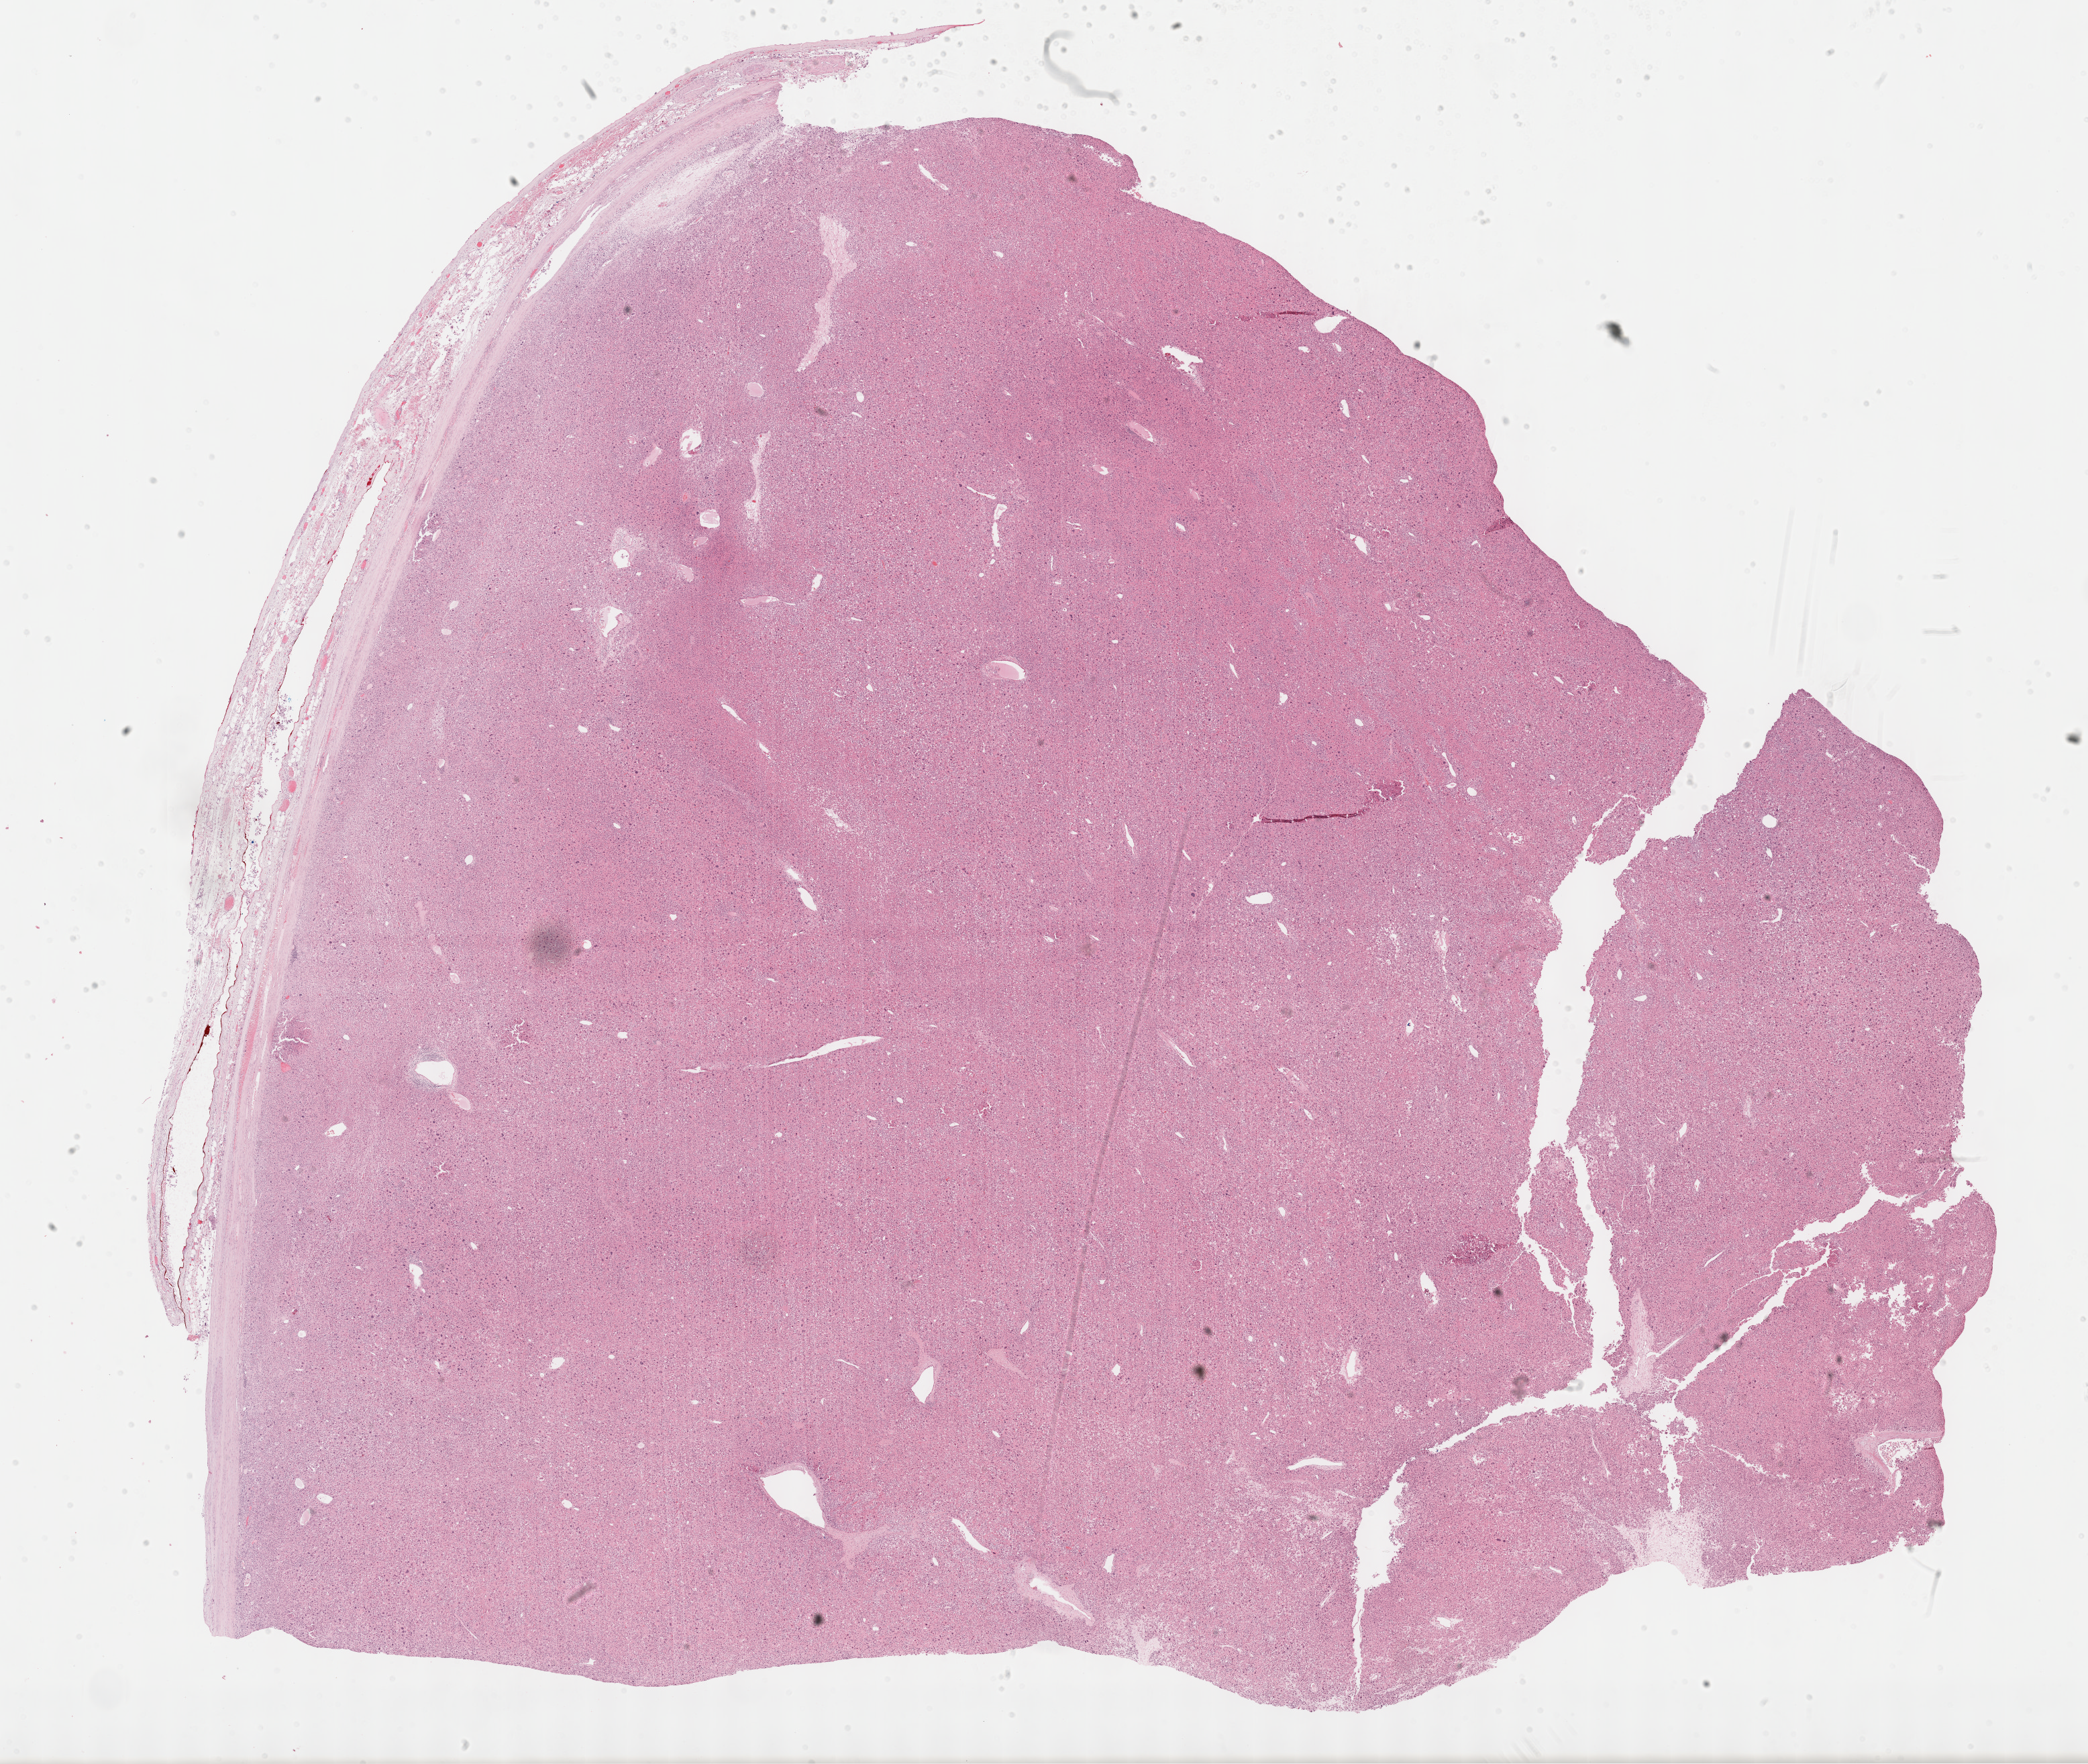
Hematoxylin and eosin (H&E) stained whole-slide image, whole scanned area (about 25.2 x 21.3 mm, slide scanned at 40x) shown as a low-resolution overview. FFPE section. Primary tumour sample from the adrenal cortex. Female patient; age at initial diagnosis 64 years.
Laterality: right. Diagnosis: Adrenal cortical carcinoma (cortex of adrenal gland).